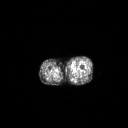
FDG PET of an extremity soft-tissue mass (from a PET/CT study), one axial slice. Position 234 of 267 along the scan axis. 3.27 mm slice thickness. 128 × 128 image matrix, field of view 700 × 700 mm. Male patient, age 48 years. Case-level facts recorded for this patient, not image findings: histological type: pleiomorphic leiomyosarcoma; grade: high; site of the primary tumour: left thigh.
Outlined on this slice (expert contour drawn on MRI and transferred to this co-registered scan by the dataset authors):
- gross tumour volume including surrounding oedema: bounding box [x1, y1, x2, y2] px = [70, 64, 74, 70]